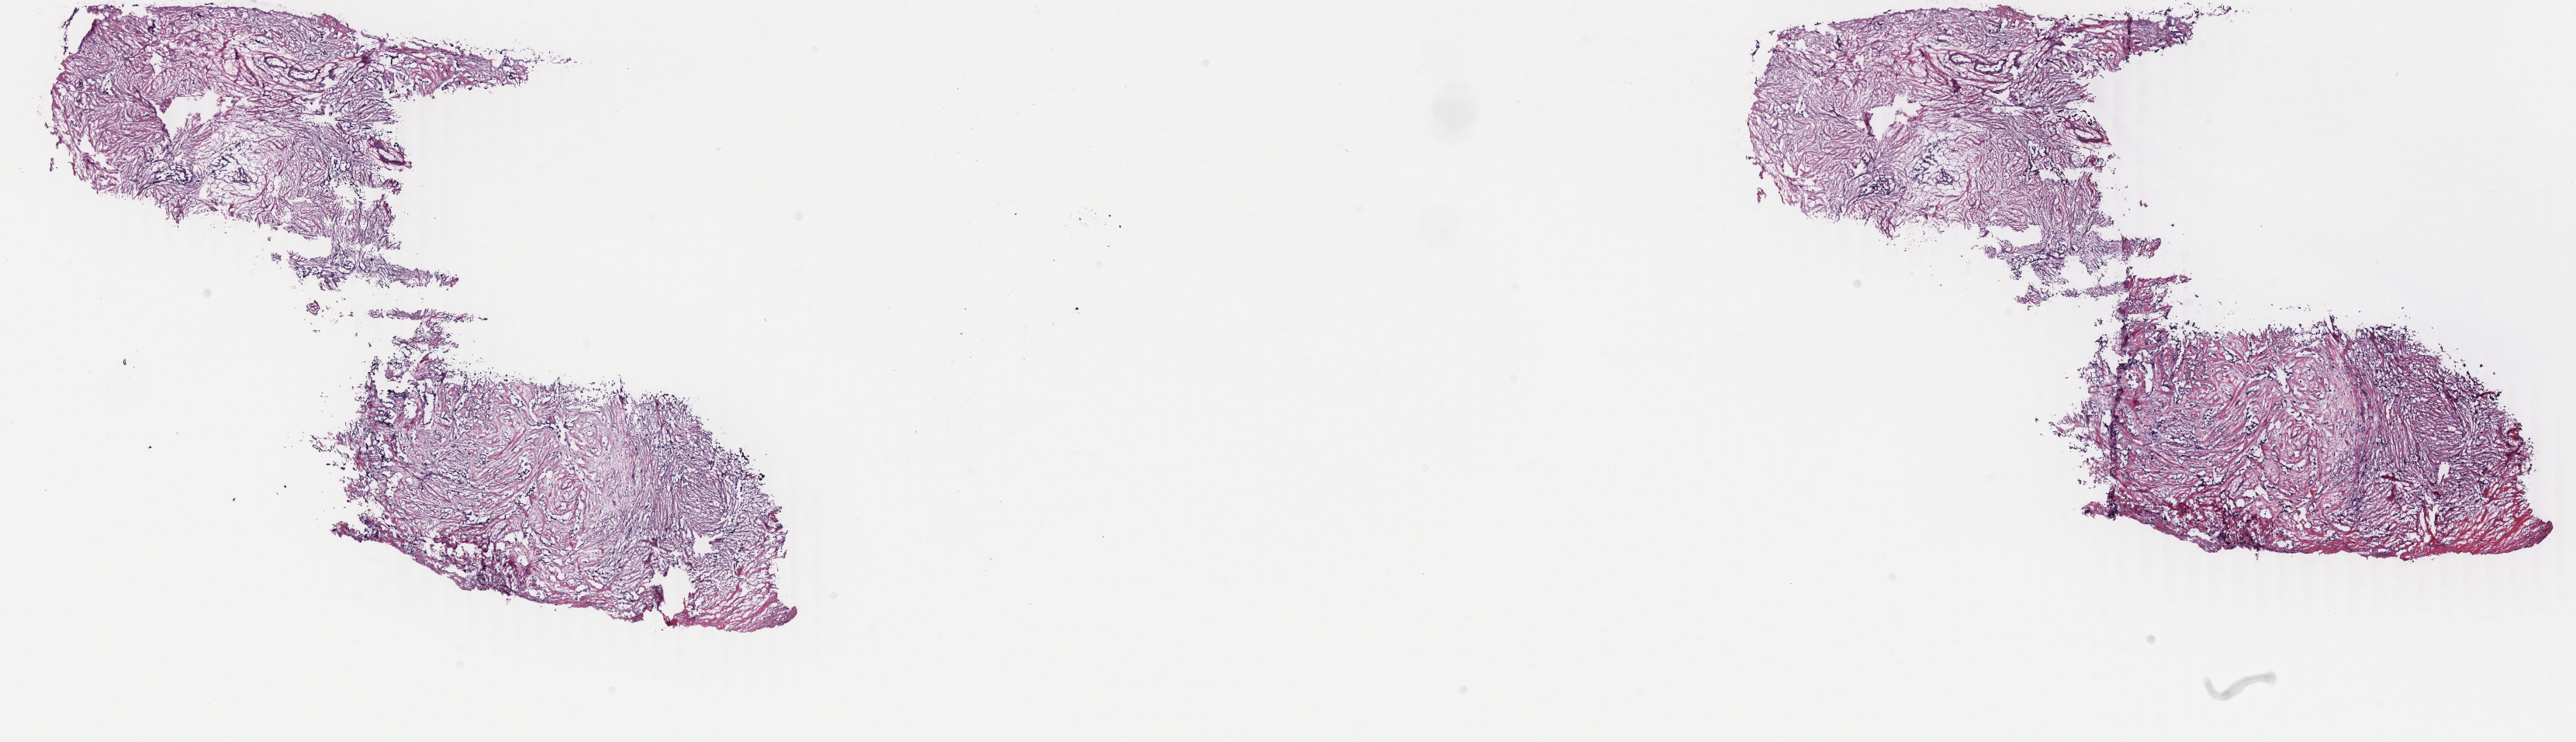
Whole-slide histology image, H&E-stained, whole scanned area (about 26.4 x 7.6 mm) shown as a low-resolution overview; frozen section; breast, primary tumour sample. Female, age 40 years at initial diagnosis.
Histologic diagnosis: Lobular carcinoma, NOS.